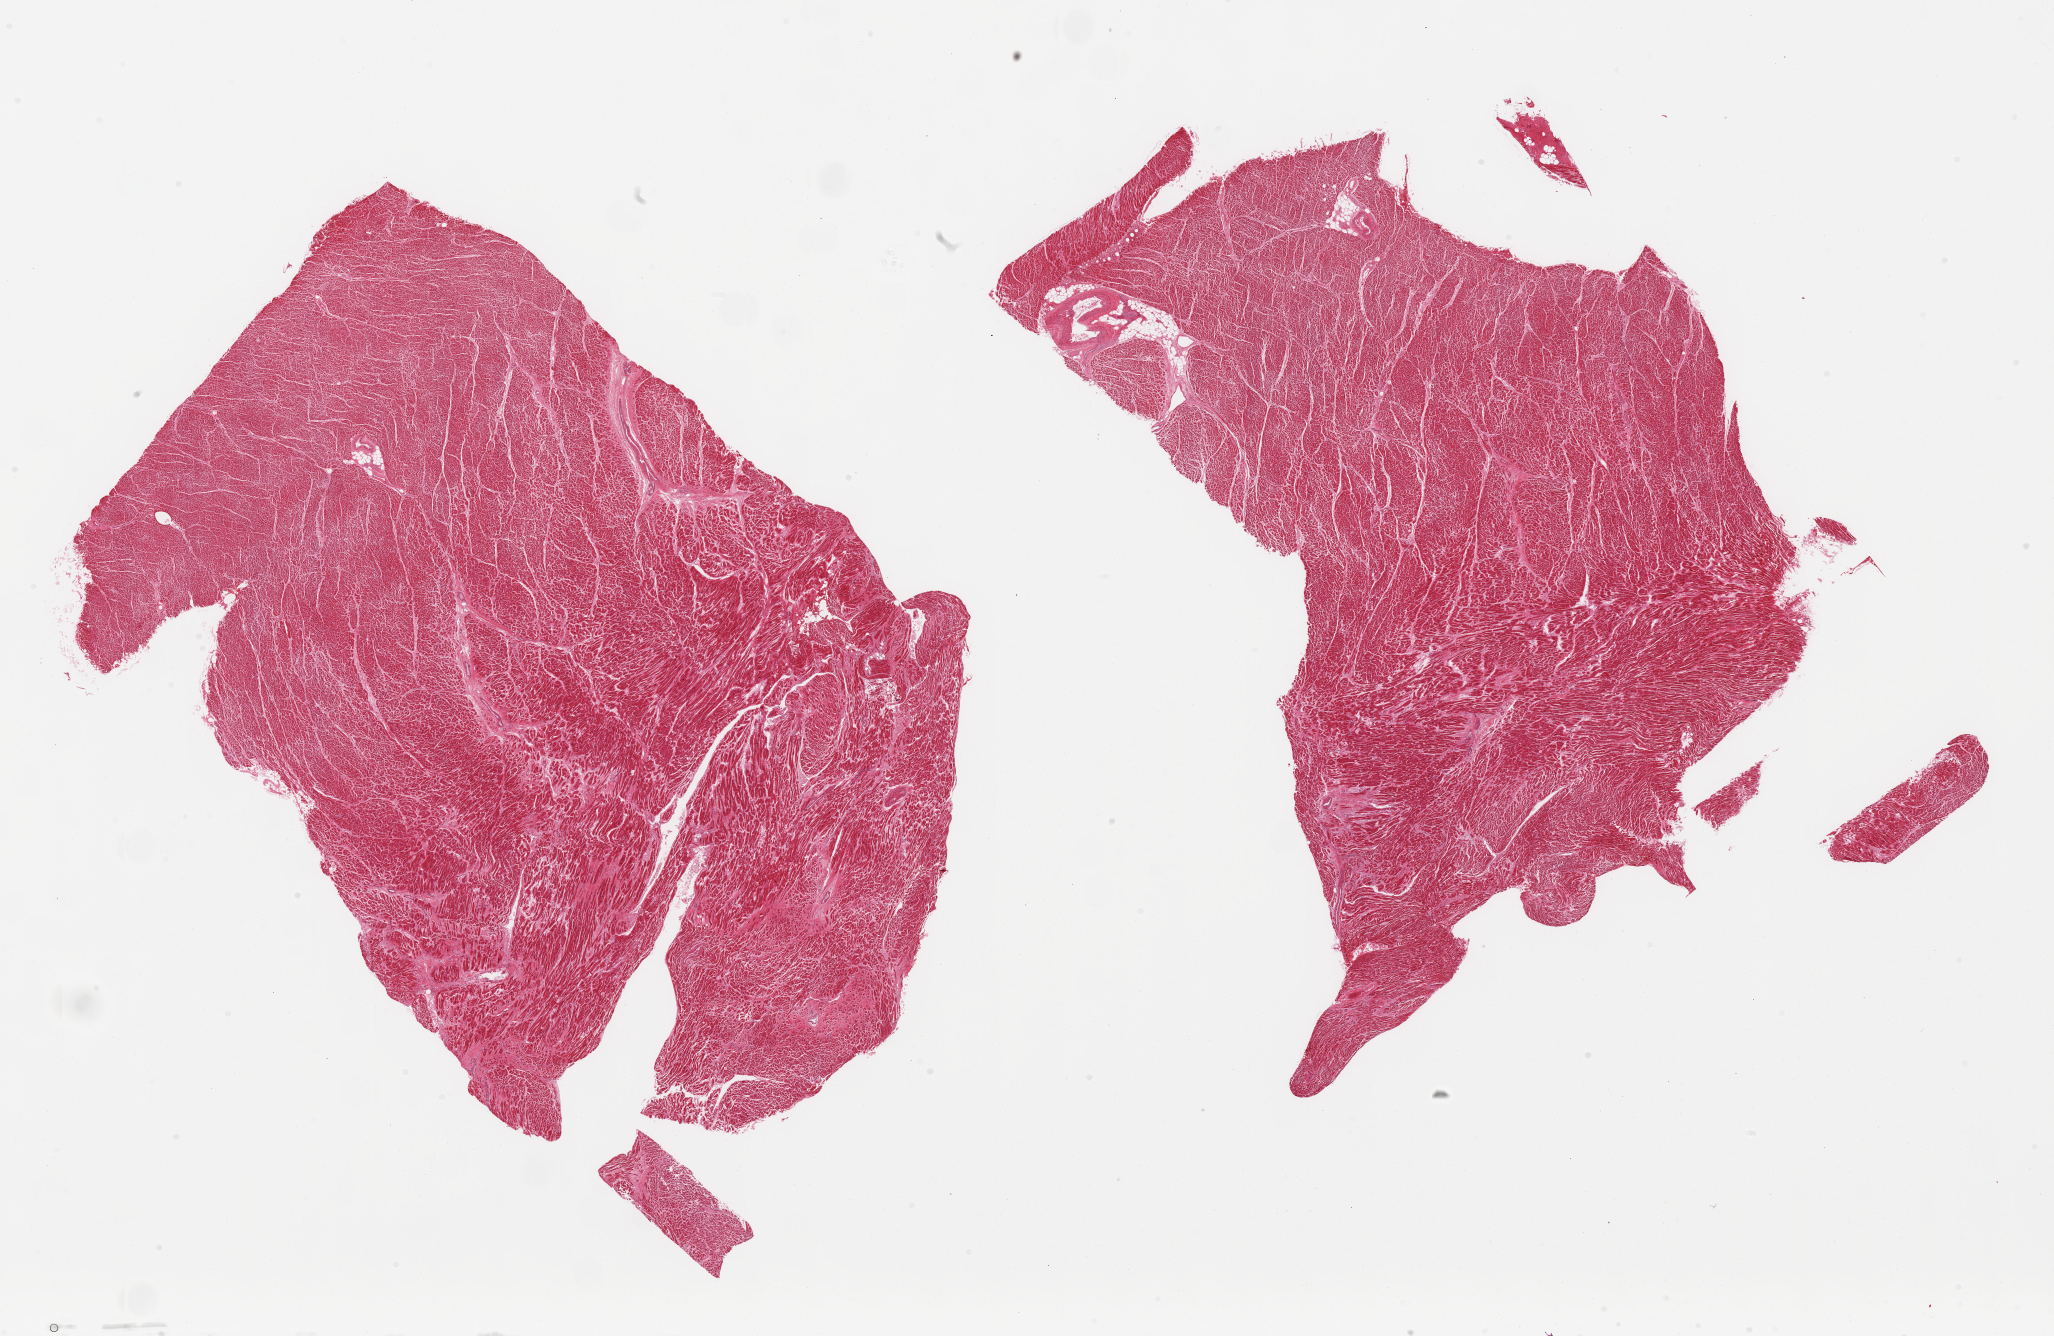
Haematoxylin and eosin whole-slide image, low-resolution overview of the scanned area, about 32.5 x 21.1 mm. PAXgene-fixed, paraffin-embedded tissue. Sampled site (target tissue): heart. Tissue donor sample. Donor: male.
Review note (as recorded): 2 pieces; patchy scars consistent with old infarcts.